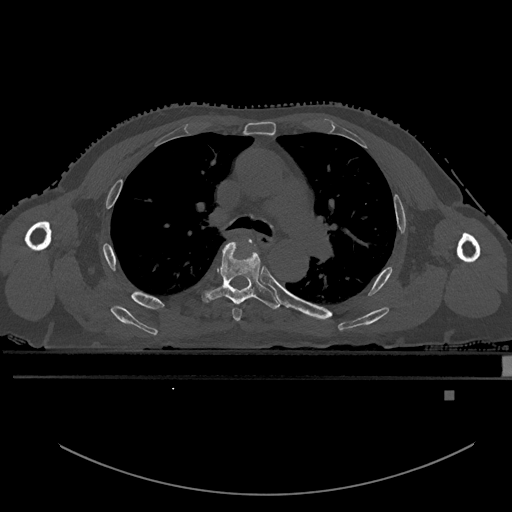
CT including the spine, one axial slice. Bone window (W 1800 / L 400 HU). 0.5 mm slice thickness. 512 × 512 image matrix, field of view 456 × 456 mm. Male patient, age 82 years. Case-level facts recorded for this patient, not image findings: primary cancer: prostate; vertebrae with lytic lesions (as recorded): T11, T9, T8, T2.
Structures marked on this image (semi-automatic segmentation, software-assisted and operator-edited):
- T4 vertebra: box from (x=233, y=237) to (x=252, y=321) px
- T5 vertebra: (x=201, y=241)–(x=280, y=310)